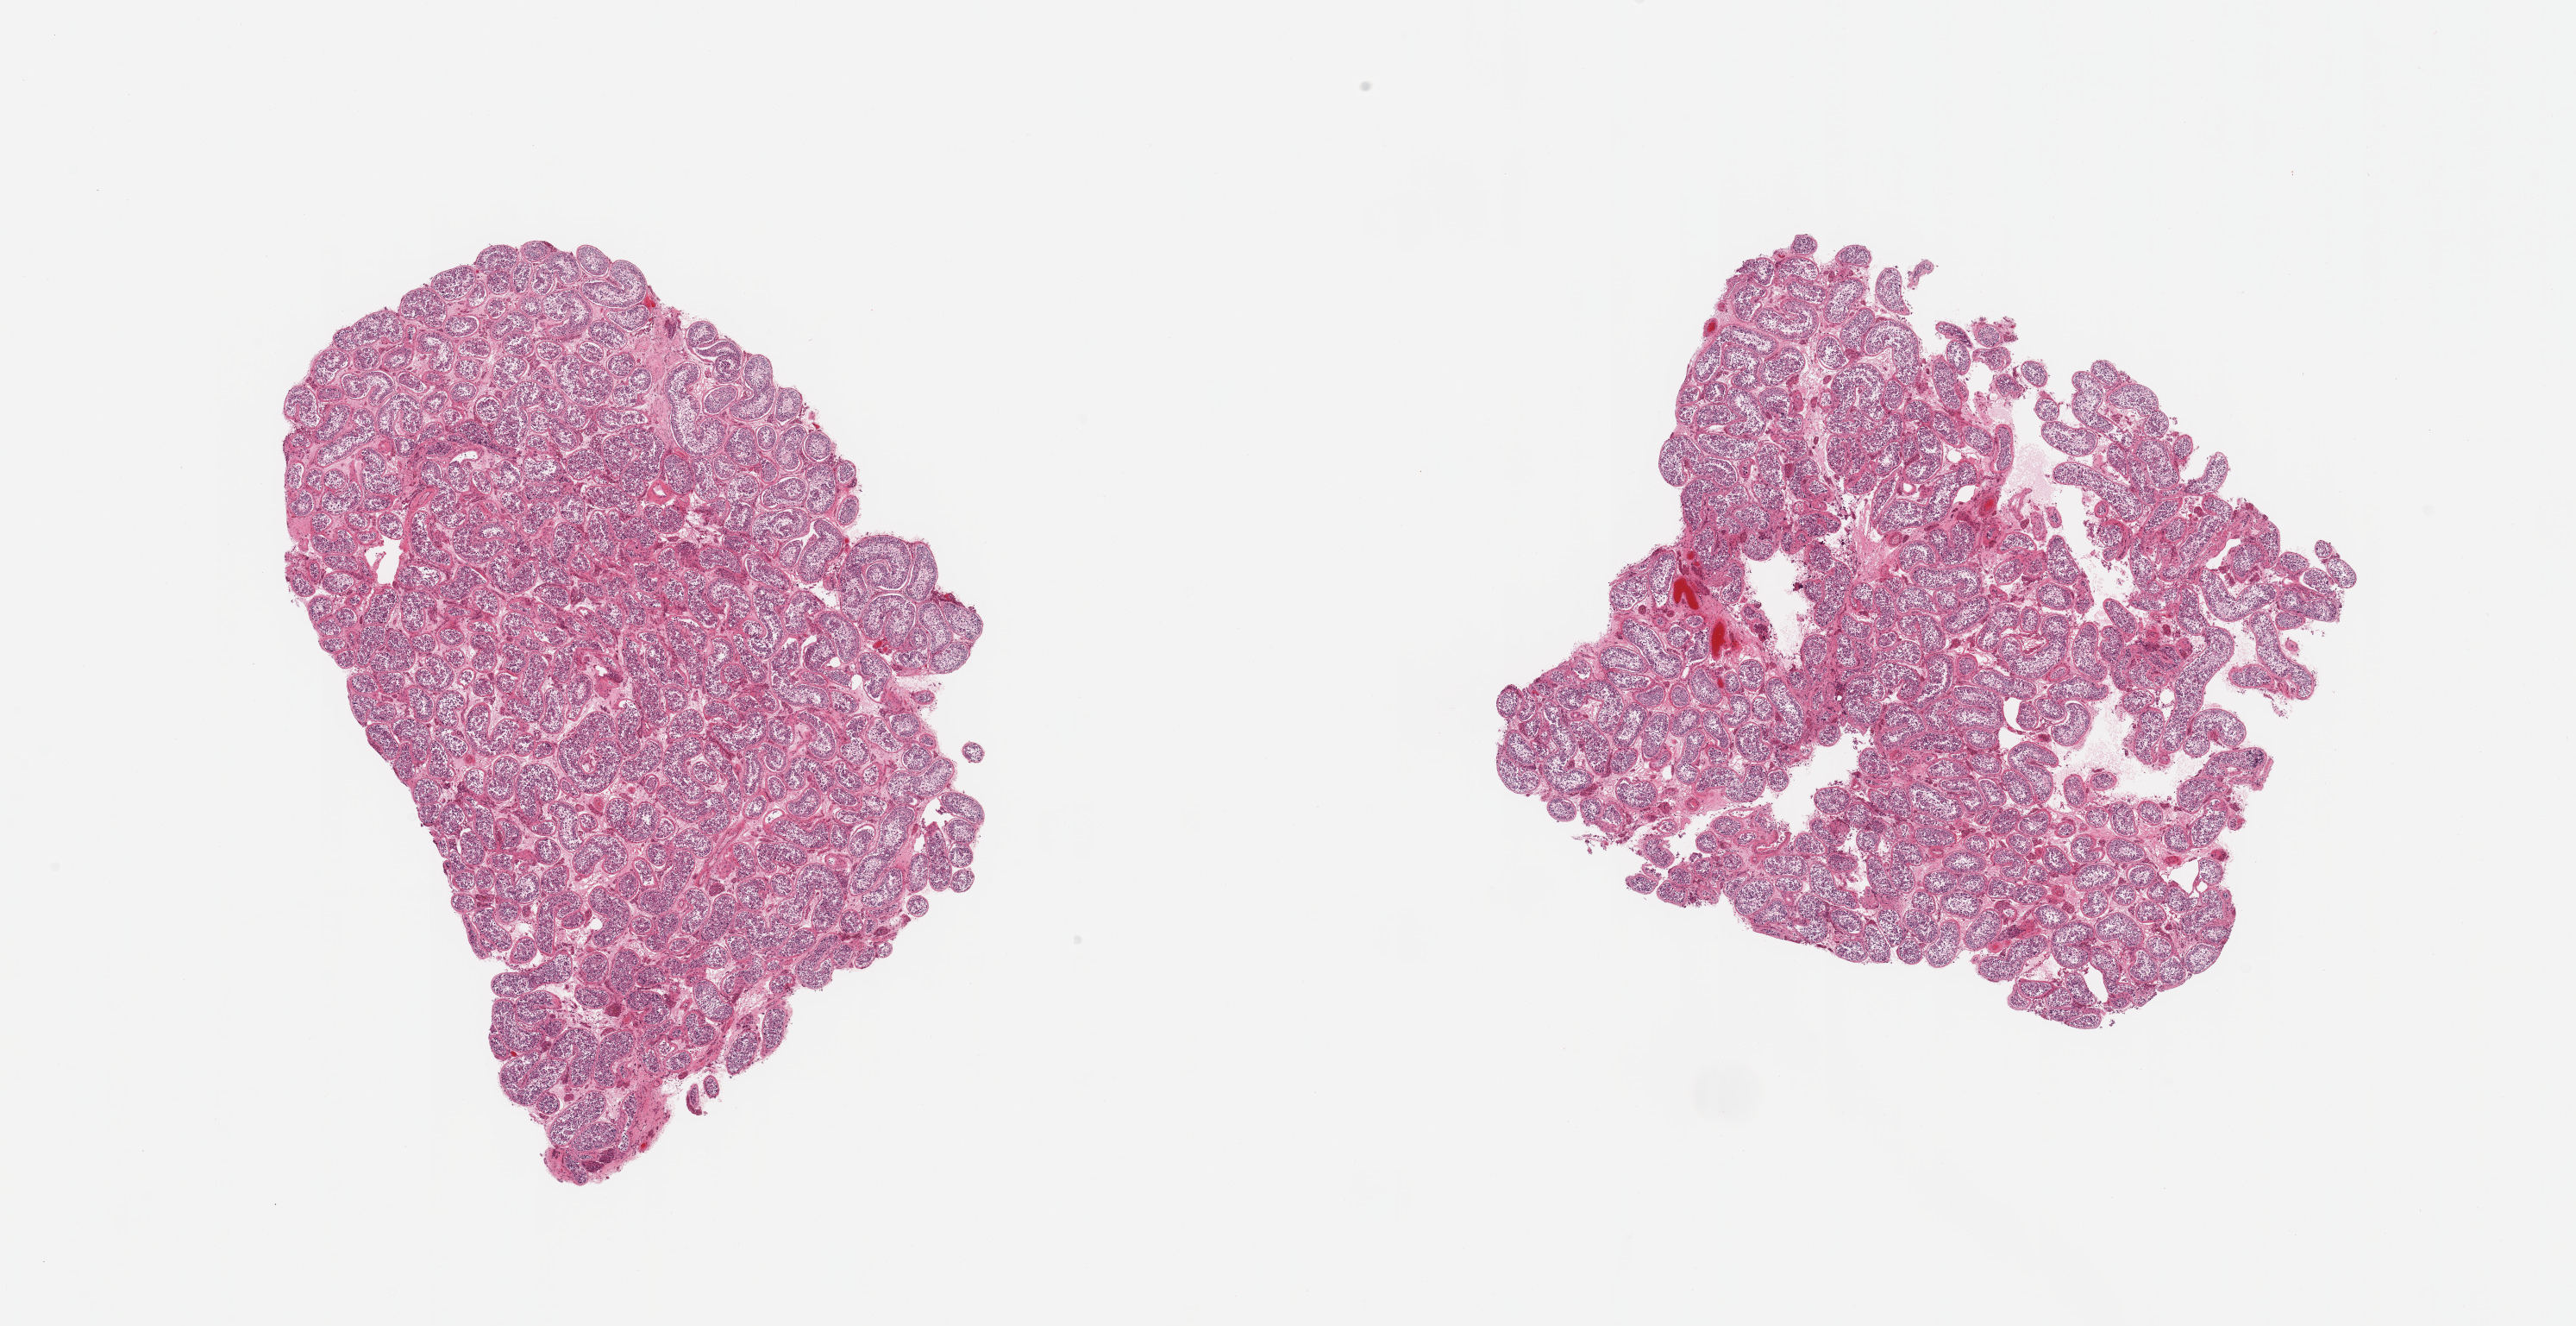
Whole-slide image, H&E stain, low-resolution overview of the scanned area, about 23.6 x 12.2 mm (slide scanned at 20x); PAXgene-fixed paraffin-embedded (PFPE) section; target tissue: testis; donor tissue sample. Male donor.
- pathologist's review note for this sample: 2 partially fragmented pieces; active spermatogenesis